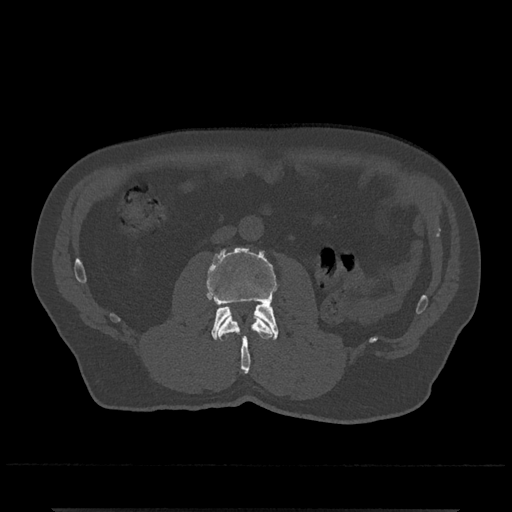
CT including the spine, one axial slice. Reconstruction kernel Br40s/3. Bone window (W 1800 / L 400 HU). 0.5 mm slice thickness. 512 × 512 image matrix, field of view 393 × 393 mm. Male patient, age 67 years. From the clinical record (not read from this slice): primary cancer: prostate.
Annotated regions visible in this slice (semi-automatically segmented with operator editing):
- L2 vertebra: box from (x=217, y=314) to (x=273, y=374) px
- L3 vertebra: (x=206, y=247)–(x=278, y=340)